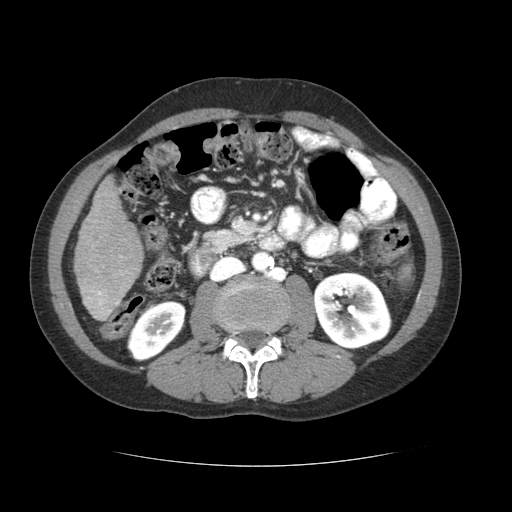
Contrast-enhanced abdominal CT (liver protocol), one axial slice; position 17 of 69 along the scan axis; soft-tissue window (W 400 / L 40 HU); 2.5 mm slice thickness; 512 × 512 image matrix. Case-level facts recorded for this patient, not image findings: diagnosis: hepatocellular carcinoma (patient treated with transarterial chemoembolisation; whether this scan precedes or follows treatment is not stated here); TNM stage (as recorded): Stage-II; Child-Pugh class: B; tumour differentiation: poorly differentiated; tumour nodularity: multinodular.
Annotated regions visible in this slice (semi-automatic segmentation, software-assisted and operator-edited):
- liver parenchyma outside the tumour (the mass and vessels are separate outlines, so this box may not span the whole liver): bounding box (x1, y1, x2, y2) in pixels: (74, 176, 144, 320)
- liver vessels: (85, 255, 123, 316)